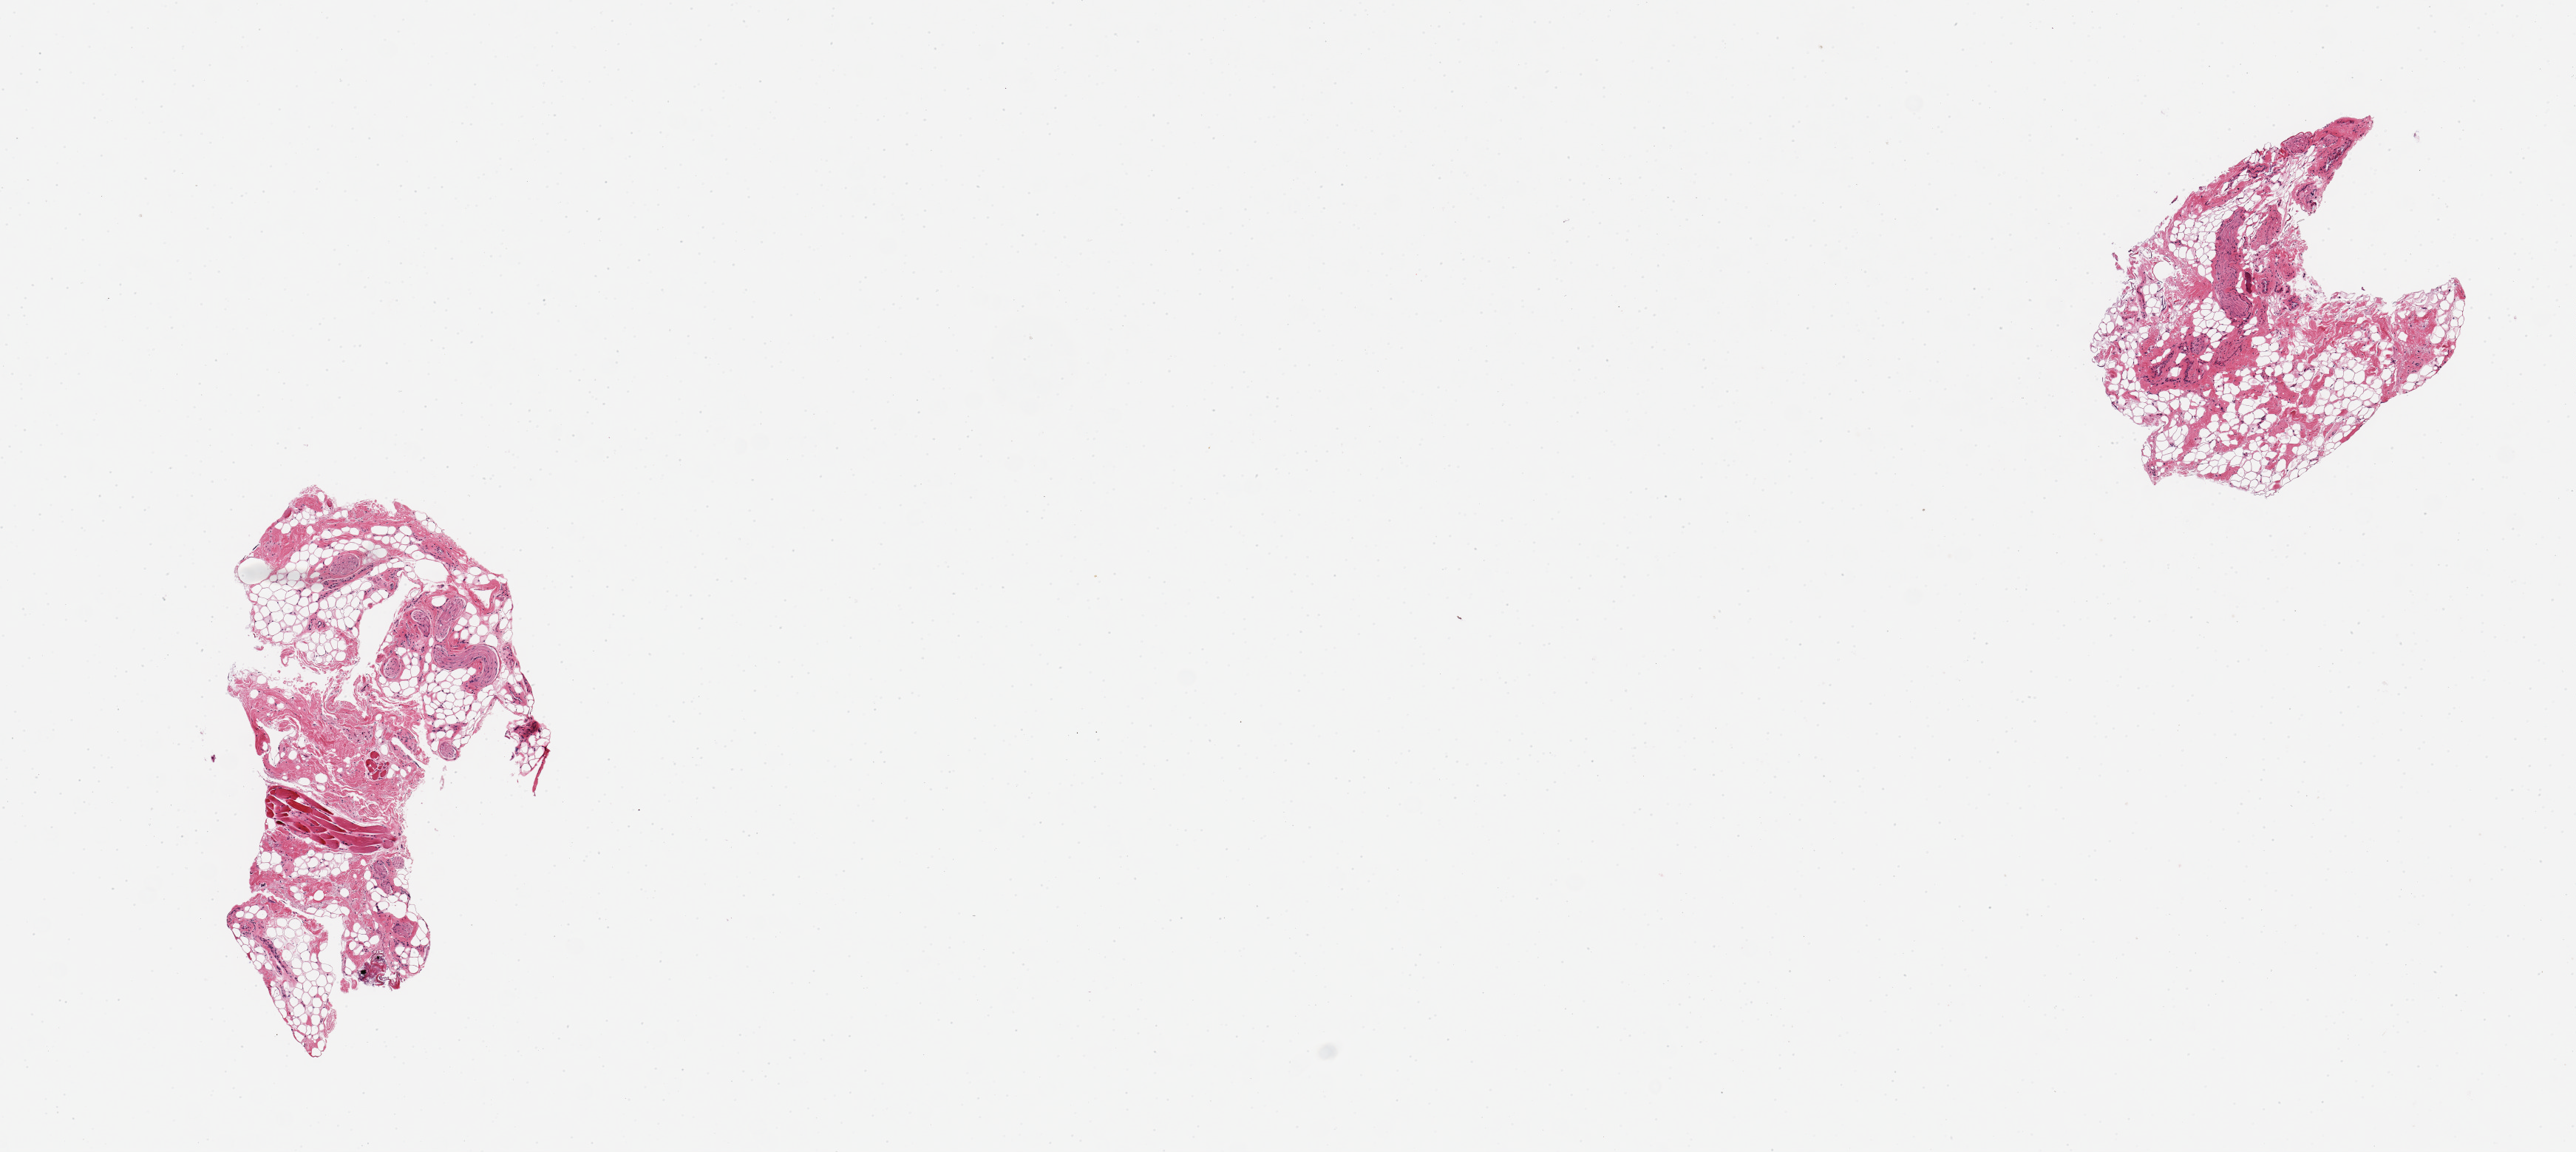
Haematoxylin and eosin whole-slide image — shown as a low-resolution overview of the whole scanned area (about 13.8 x 6.2 mm); PAXgene-fixed, paraffin-embedded tissue; section of minor salivary gland (target tissue); tissue donor sample. Donor sex: male.
* review note (as recorded): 2 pieces, no glandular tissue, mesenchymal elements only